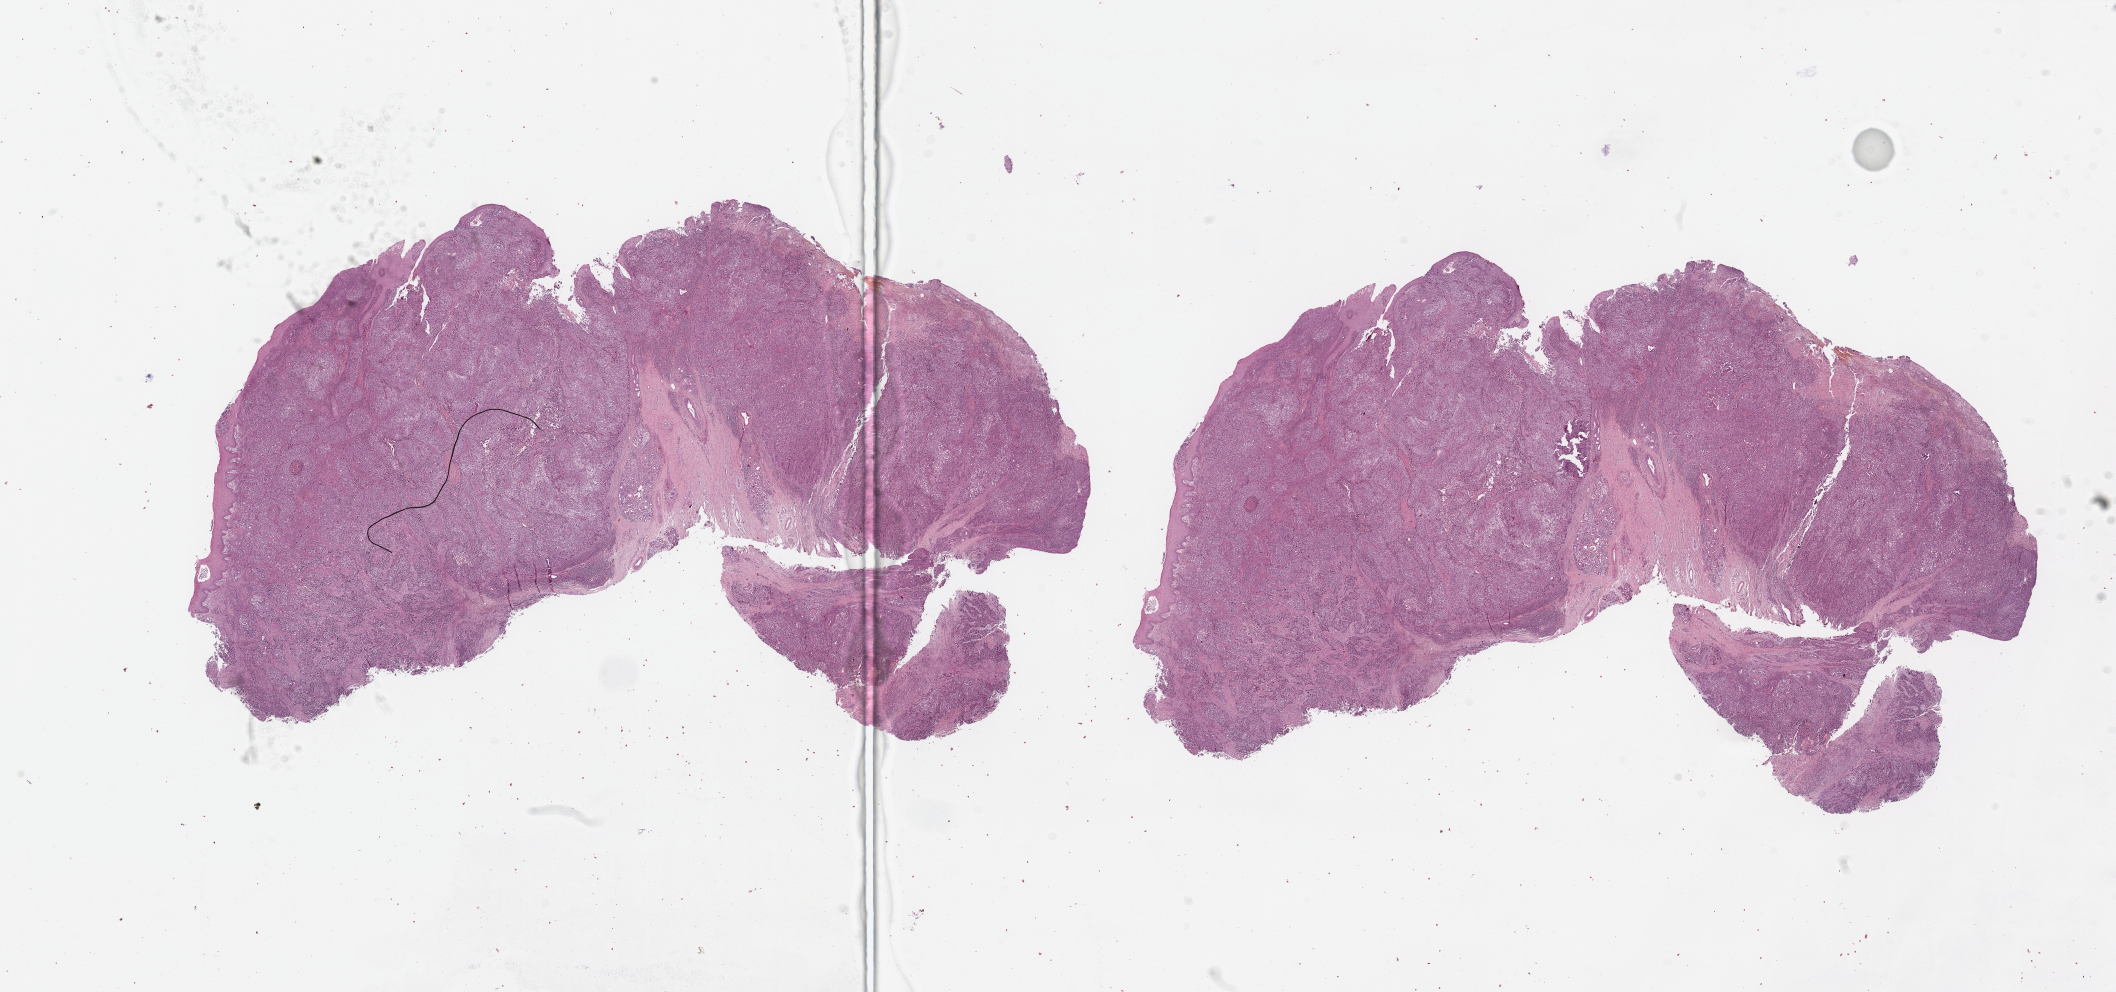
H&E-stained whole-slide image, low-resolution overview of the scanned area, about 33.5 x 15.7 mm (from a 20x scan), tumour tissue sample, sampled site: larynx. Patient: male, age 64 years. Composition of this section per pathologist review: tumour nuclei 80%, necrosis 3%.
Diagnosis: Squamous cell carcinoma, NOS.